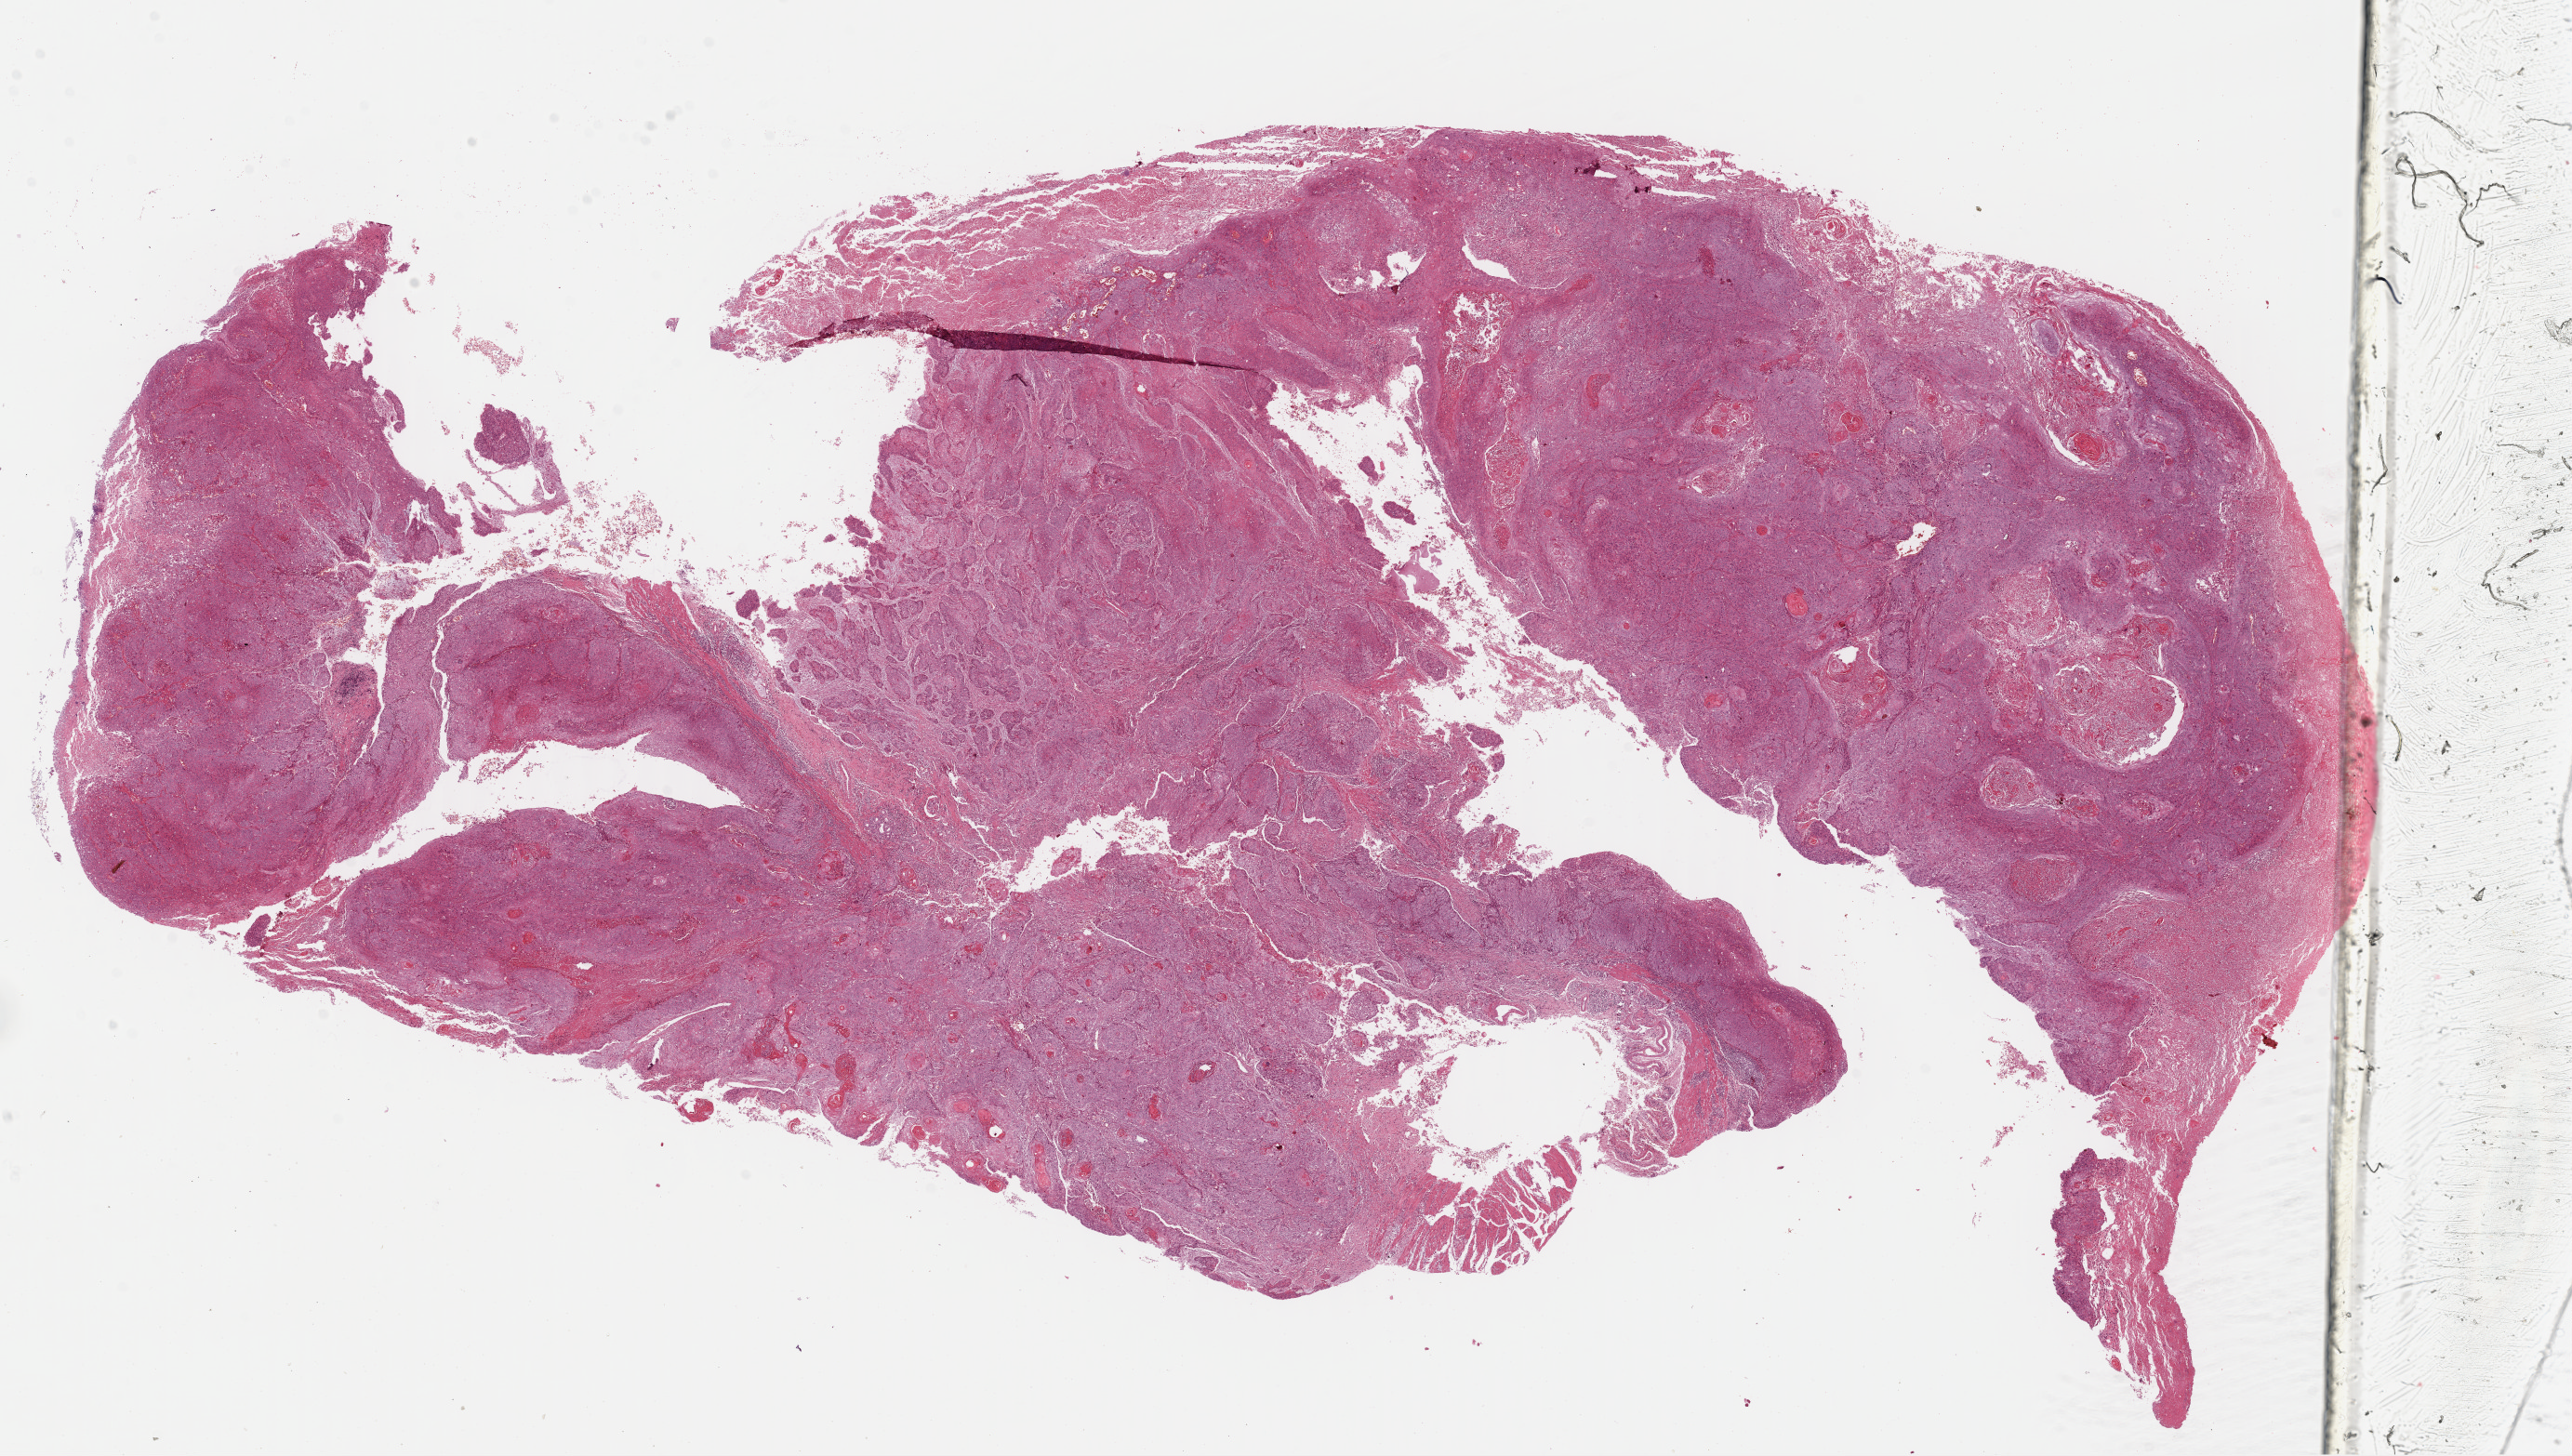
Whole-slide histology image, Hematoxylin and eosin (H&E) stained — a low-resolution overview of the entire scanned area, about 21.7 x 12.3 mm, formalin-fixed paraffin-embedded (FFPE) diagnostic section, primary tumour sample from the esophagus. Male, age 46 years at initial diagnosis. Histologic grade: G1 (well differentiated).
Pathologic diagnosis: Squamous cell carcinoma, NOS. AJCC pathologic stage: IIA (6th edition).